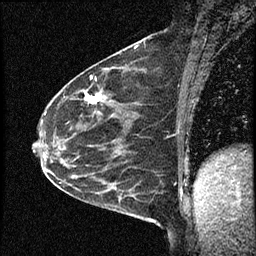
Breast MRI (dynamic contrast-enhanced), one sagittal slice. Slice 32 of 60 in the series (ordered by position). Dynamic contrast-enhanced study with each time point stored as its own series, time point 2 of 4 at this slice position (early post-contrast, ordered by acquisition time). 1.5 T. TE 4.2 ms, TR 17.6 ms. 2 mm slice thickness. 256 × 256 image matrix, field of view 200 × 200 mm. Patient: female, 53 years. From the clinical record (not read from this slice): setting: breast cancer imaged before/during neoadjuvant chemotherapy; receptor status: HR-positive, HER2-negative.
Structures marked on this image (semi-automatically segmented with operator editing):
- analysis volume of interest (the breast-tissue region the enhancement analysis was run in; not a lesion): bounding box <42,69,146,199> (left, top, right, bottom; pixels)
- tumour enhancement mask (voxels above the 100 % enhancement threshold inside the analysis volume of interest): <84,92,104,104>